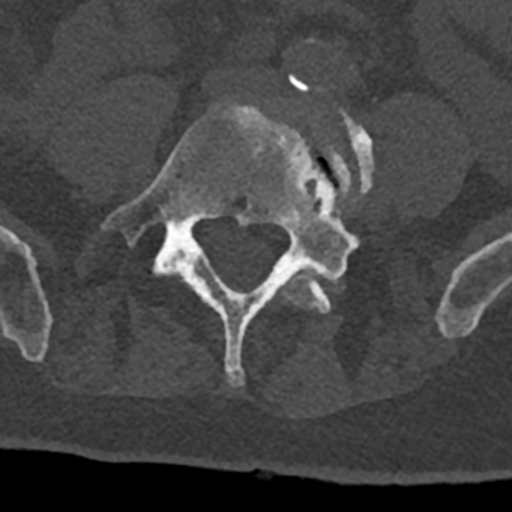
CT including the spine, one axial slice; slice 212 of 797 in the series (ordered by position); 120 kVp; bone window (W 1800 / L 400 HU); 512 × 512 image matrix. Male patient, age 74 years. From the clinical record (not read from this slice): primary cancer: renal; vertebrae with lytic lesions (as recorded): T10, L1, L2, L3, L4, L5.
Annotated regions visible in this slice (semi-automatically segmented with operator editing):
- L4 vertebra: bounding box [x1, y1, x2, y2] px = [178, 85, 374, 313]
- L5 vertebra: [101, 100, 357, 387]